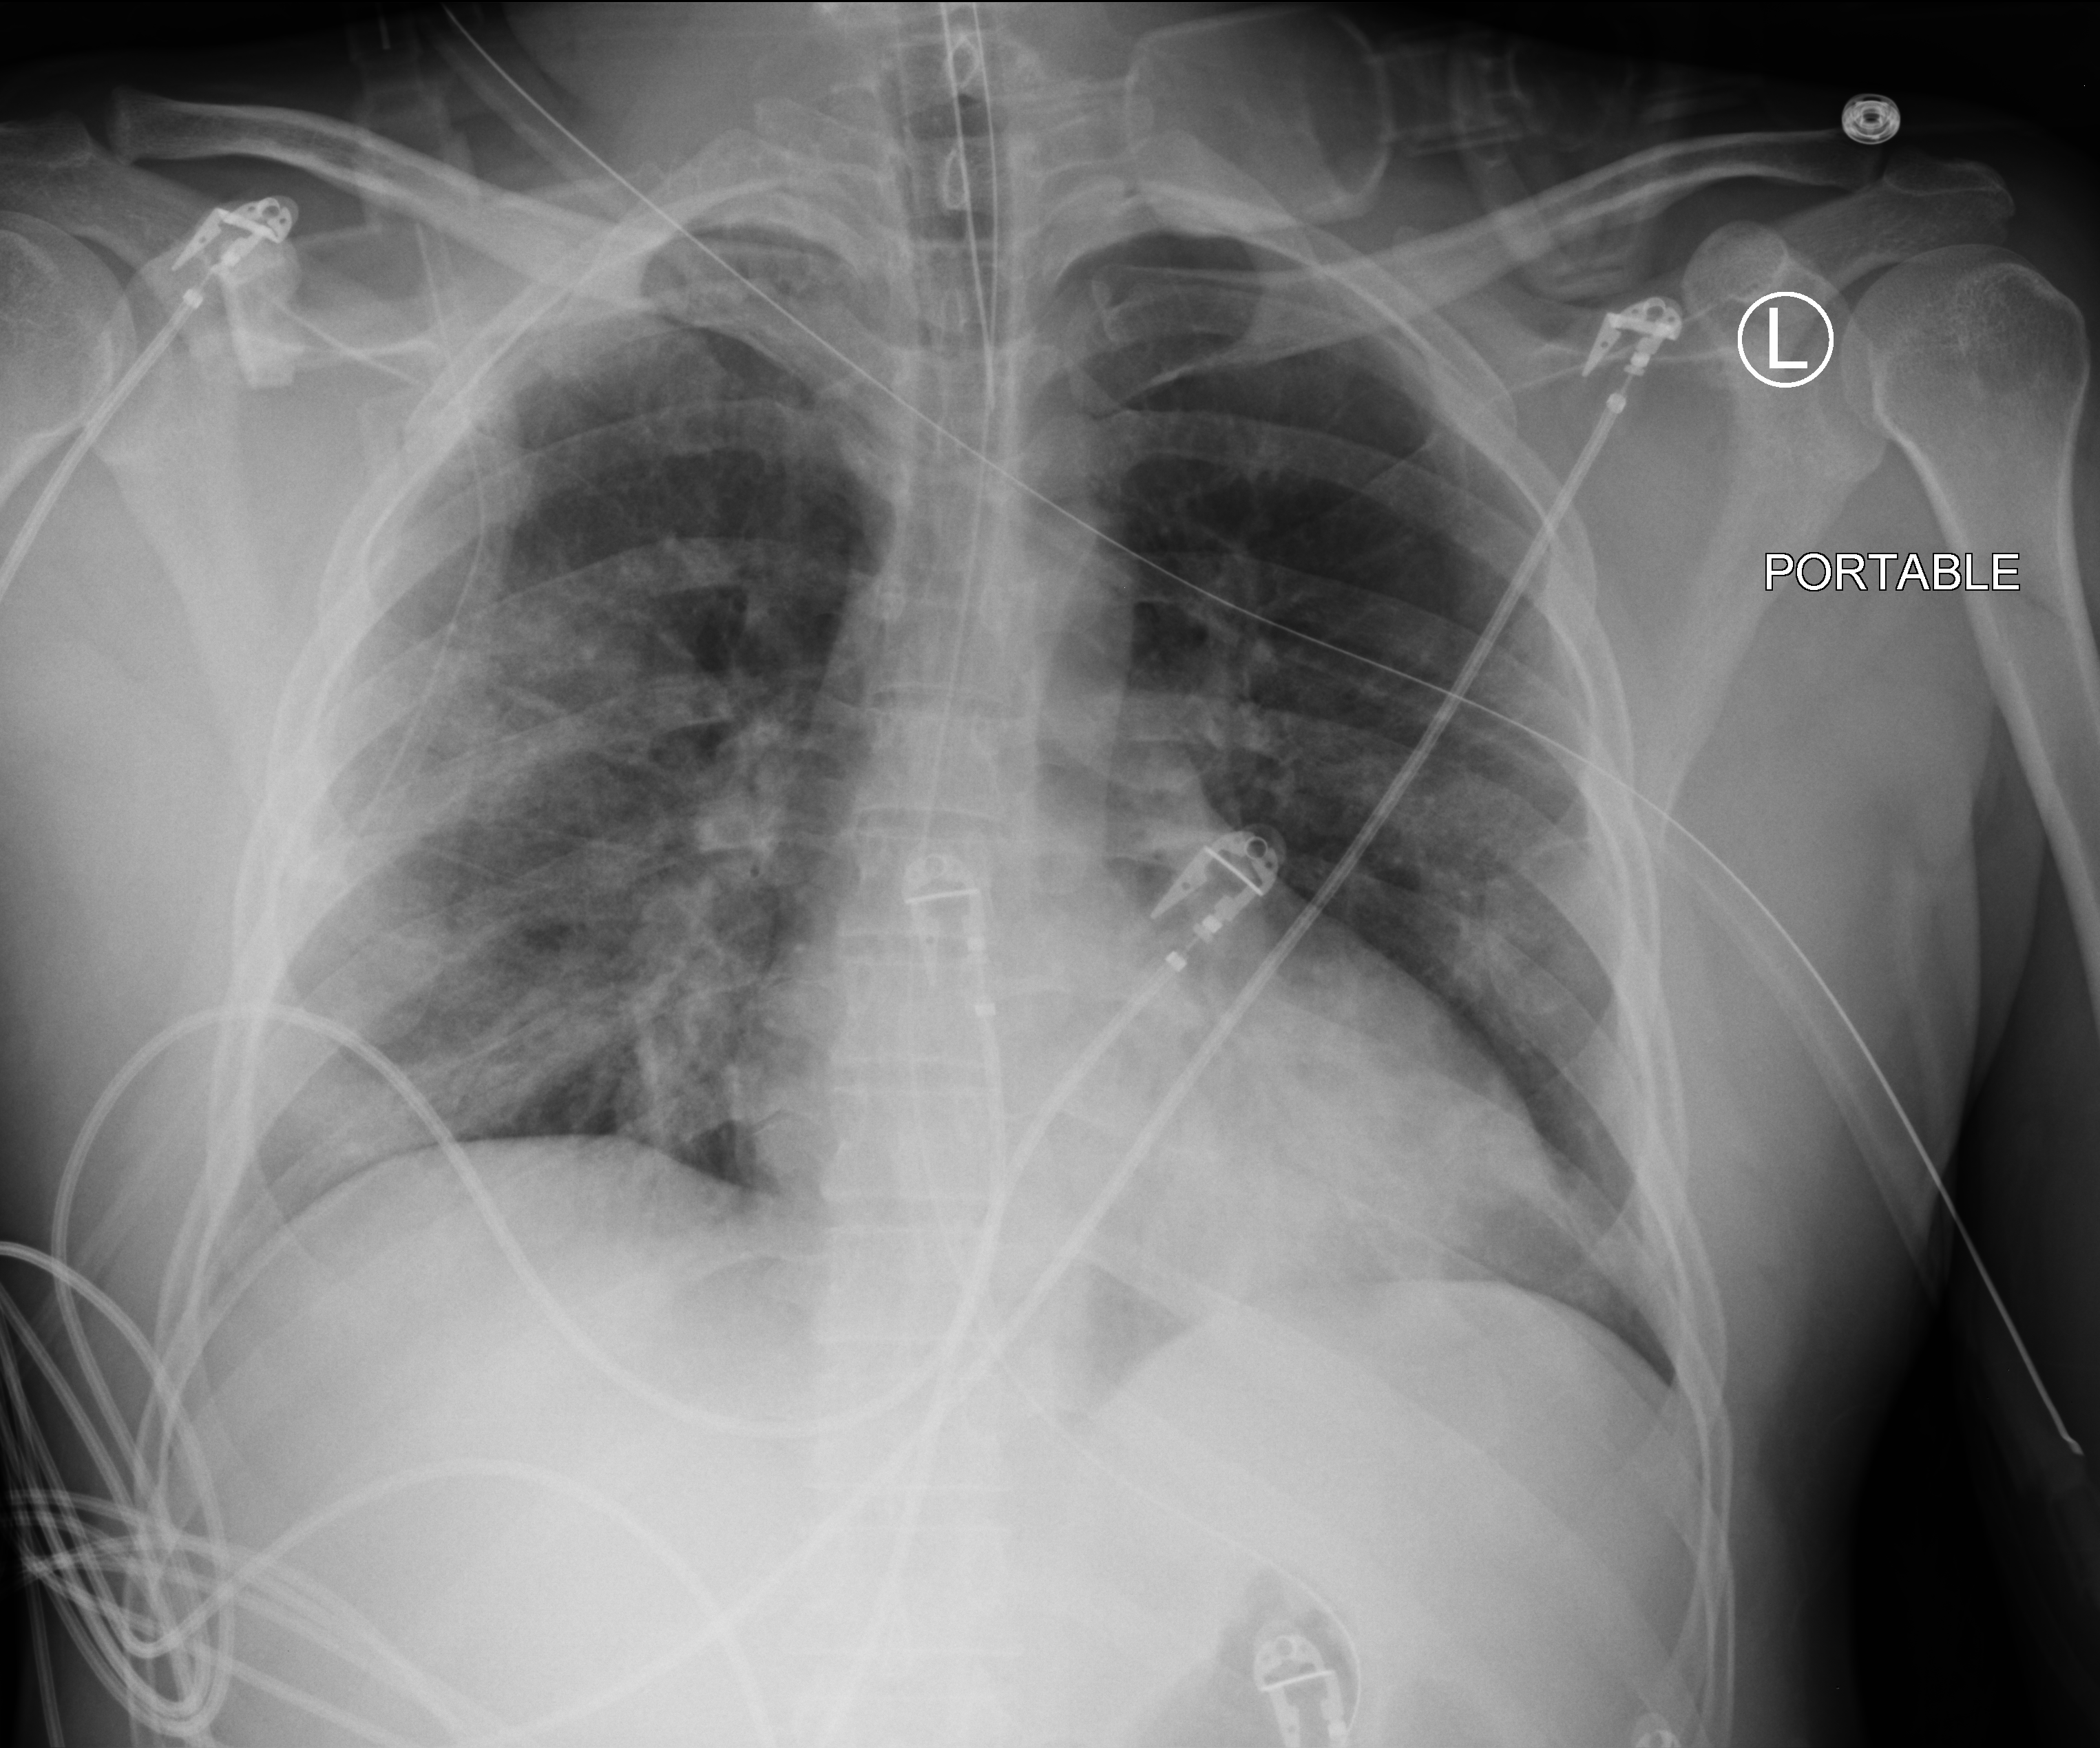
Bedside chest radiograph (computed radiography); anteroposterior (AP) projection. Patient hospitalised with COVID-19; male, aged 18–59 years.
From the hospital-stay record, not from the radiograph (when in the stay this image was taken is not recorded): admitted to intensive care during this hospital stay: yes; mechanically ventilated during this hospital stay: yes.